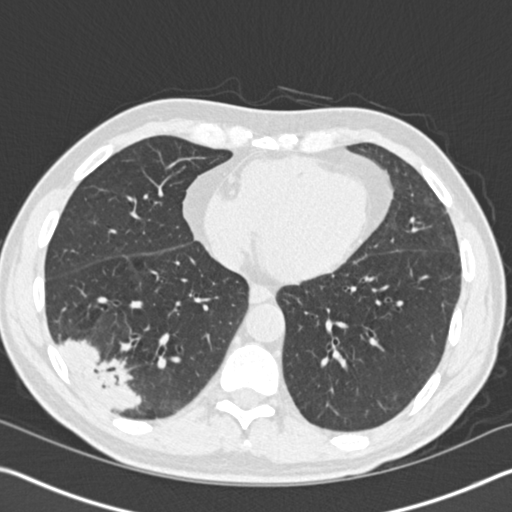
Axial slice from a low-dose chest CT screening exam. Baseline annual screen. Lung window (W 1500 / L -600 HU). 2 mm slice thickness. Standard (soft-tissue) reconstruction kernel (B30f). 512 × 512 image matrix. Male, age 61 years at enrolment.
Expert-annotated lung lesion, bounding box [x1, y1, x2, y2] px = [35, 308, 151, 420]. Screening reader's record for this exam (one nodule recorded; not confirmed to be the boxed lesion): non-calcified nodule or mass ≥4 mm, right lower lobe, 52 × 36 mm, spiculated (stellate) margins, soft tissue attenuation. Official screen result: positive, change unspecified: nodule(s) >= 4 mm or enlarging nodule(s), mass(es), or other non-specific abnormalities suspicious for lung cancer. Lung cancer was diagnosed 392 days after this screen (after the second annual screen): bronchiolo-alveolar adenocarcinoma, NOS, right lower lobe, moderately differentiated (G2), stage IIIB (AJCC 6th edition), 90 mm at pathology.